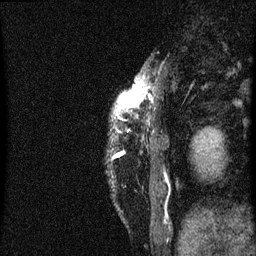
Breast MRI (dynamic contrast-enhanced), one sagittal slice; position 10 of 60 along the scan axis; dynamic contrast-enhanced series, image 2 of 3 at this slice position (ordered by acquisition); 1.5 T; TE 4.2 ms, TR 8 ms; 2 mm slice thickness; 256 × 256 image matrix, field of view 180 × 180 mm. Patient: female, 38 years.
Annotated regions visible in this slice (semi-automatic segmentation, software-assisted and operator-edited):
- analysis volume of interest (the breast-tissue region the enhancement analysis was run in; not a lesion): bounding box [x1, y1, x2, y2] px = [118, 90, 141, 117]
- tumour enhancement mask (voxels above the 70 % enhancement threshold inside the analysis volume of interest): [122, 90, 137, 109]